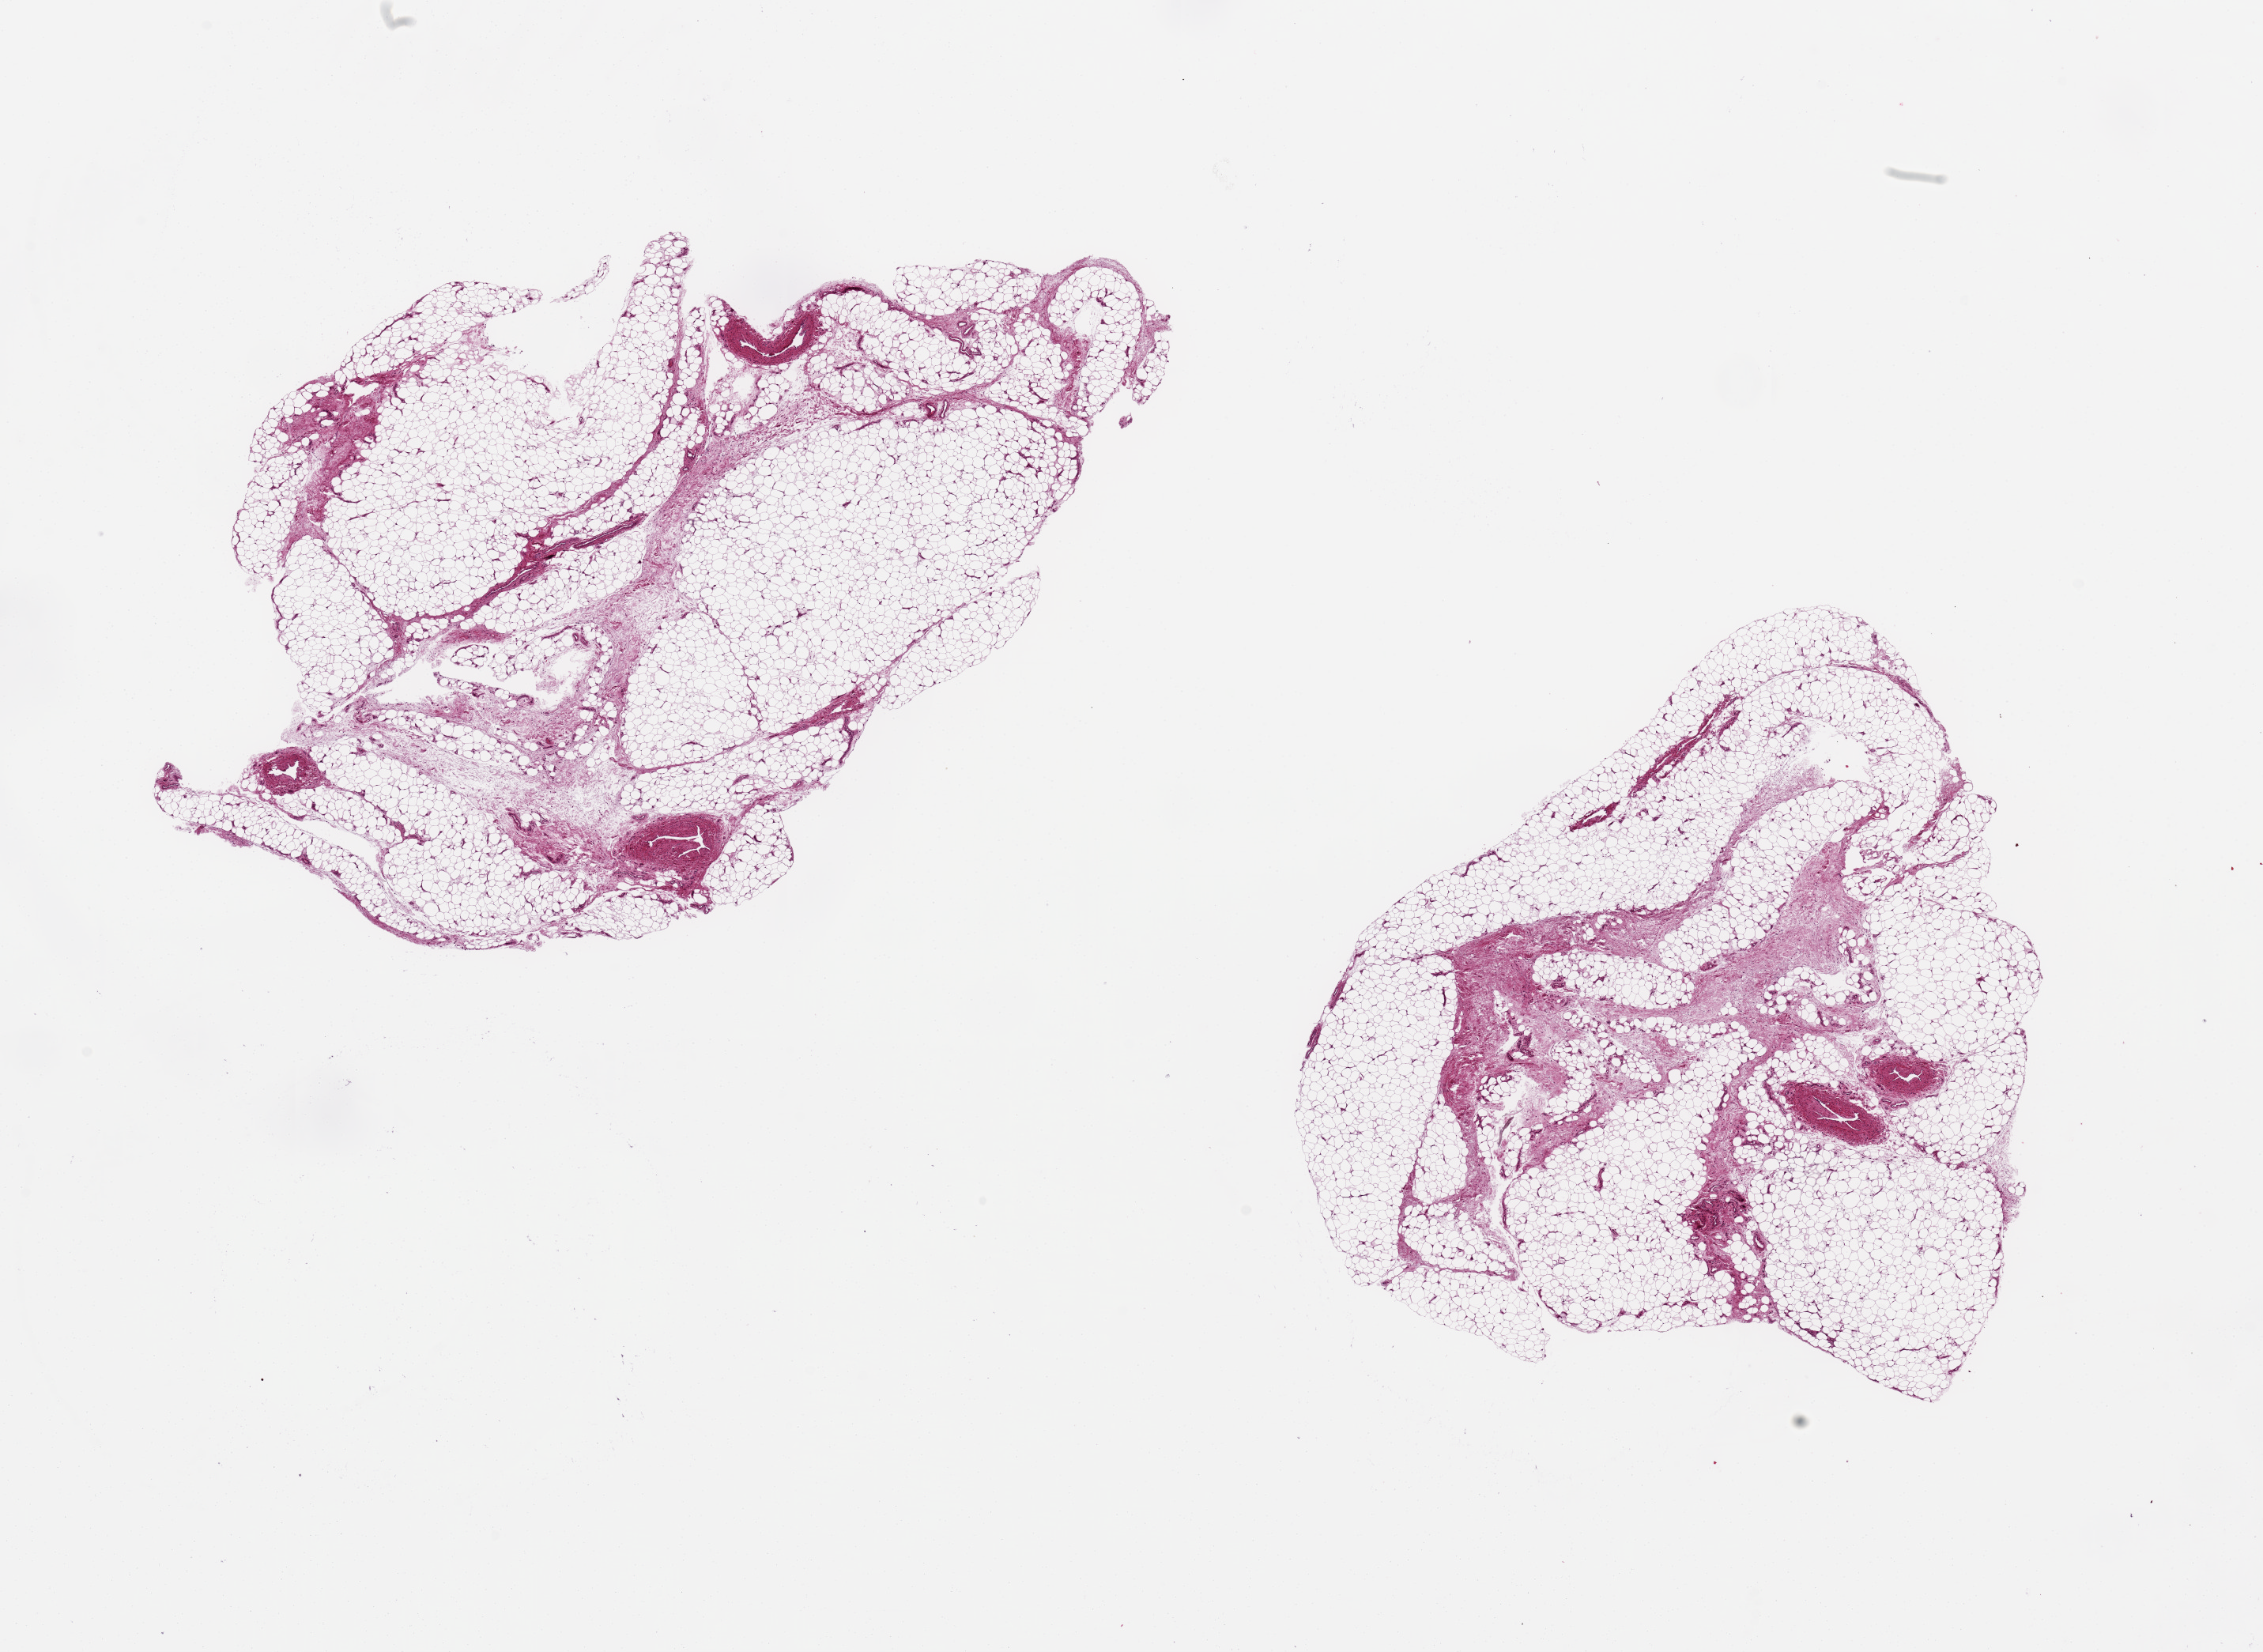
Hematoxylin and eosin (H&E) whole-slide image, brightfield — low-resolution overview of the scanned area, about 22.6 x 16.5 mm. PAXgene-fixed paraffin-embedded (PFPE) section. Target tissue: adipose tissue. Donor tissue sample. Donor sex: male.
• pathologist's review note for this sample: 2 ~7x7mm pieces, well-fixed